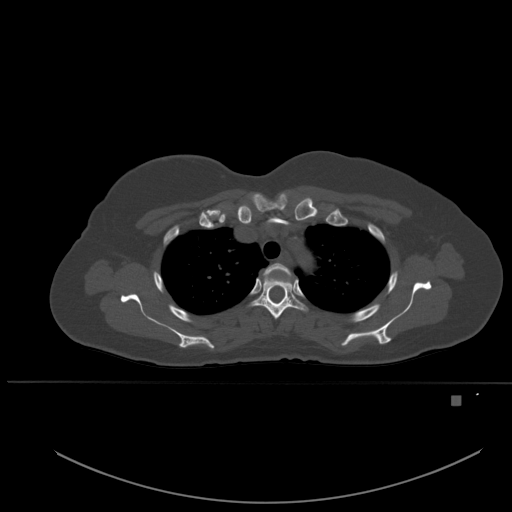
CT including the spine, one axial slice; bone window (W 1800 / L 400 HU); 1.5 mm slice thickness; 512 × 512 image matrix, field of view 443 × 443 mm. Female patient, age 49 years. Case-level facts recorded for this patient, not image findings: primary cancer: breast; vertebrae with lytic lesions (as recorded): L3, T12, L4.
Annotated regions visible in this slice (semi-automatic segmentation, software-assisted and operator-edited):
- T2 vertebra: box from (x=263, y=263) to (x=291, y=276) px
- T3 vertebra: (x=250, y=274)–(x=308, y=319)